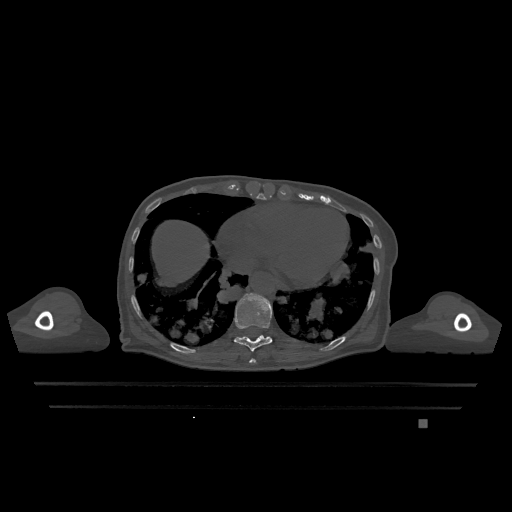
CT including the spine, one axial slice. Position 636 of 1317 along the scan axis. Bone window (W 1800 / L 400 HU). 0.5 mm slice thickness. 512 × 512 image matrix. Female patient, age 74 years. From the clinical record (not read from this slice): primary cancer: lung; vertebrae with lytic lesions (as recorded): T1, T4, T5, T6, L4, L5.
Annotated regions visible in this slice (semi-automatically segmented with operator editing):
- T10 vertebra: box from (x=234, y=293) to (x=273, y=352) px
- T9 vertebra: (x=249, y=359)–(x=257, y=363)